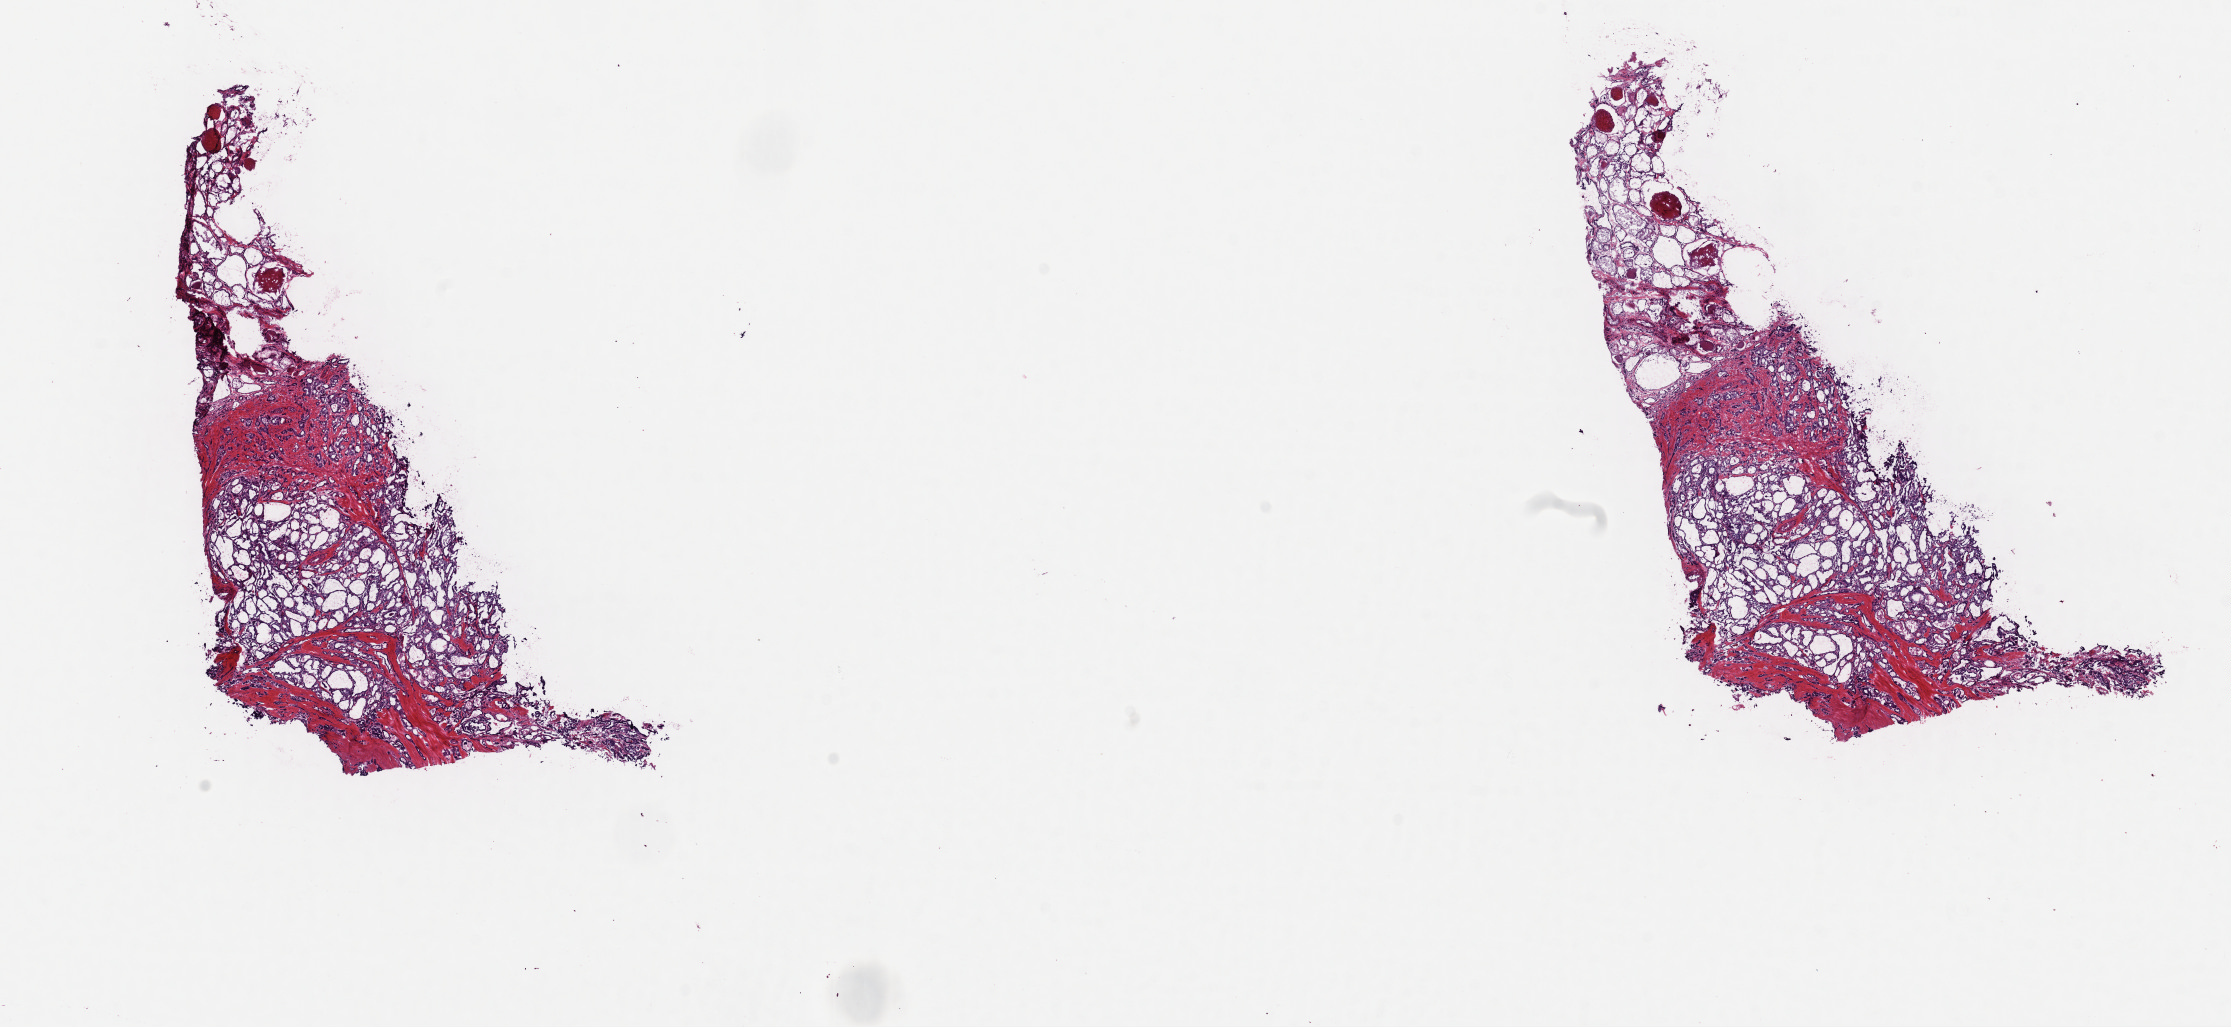
Whole-slide histology image, H&E-stained — shown as a low-resolution overview of the whole scanned area (about 17.6 x 8.1 mm), frozen section from the top of the tissue portion, primary tumour sample from the thyroid. Patient: female, age at initial diagnosis 56 years. Composition of this section per pathologist review: tumour cells 60%, tumour nuclei 85%, normal cells 15%, stromal cells 25%, necrosis 0%. Infiltration values recorded for this section: lymphocyte infiltration 2%, monocyte infiltration 0%, neutrophil infiltration 0%.
• AJCC pathologic stage: III (7th edition)
• diagnosis: Papillary carcinoma, follicular variant